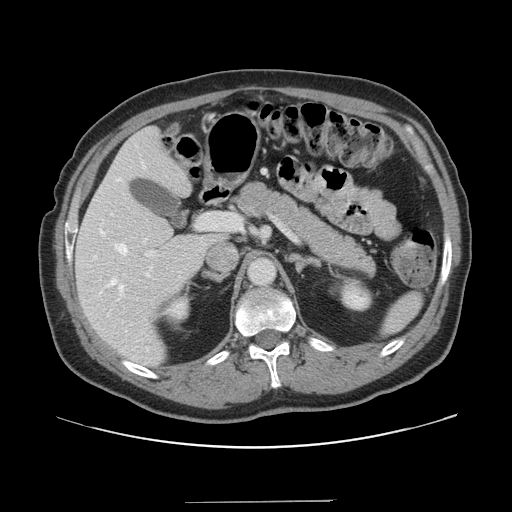
Contrast-enhanced abdominal CT, one axial slice; slice 87 of 151 in the series (ordered by position); 120 kVp; soft-tissue window (W 400 / L 40 HU); 2.5 mm slice thickness; 512 × 512 image matrix, field of view 399 × 399 mm. Male patient, age 63 years. From the clinical record (not read from this slice): diagnosis: colorectal cancer liver metastases, imaged before liver resection.
Annotated regions visible in this slice (manually delineated by an expert):
- hepatic veins: bounding box <100,162,149,333> (left, top, right, bottom; pixels)
- liver: <76,129,221,367>
- planned liver remnant (the part of the liver to remain after resection): <76,129,221,367>
- portal vein (with intrahepatic branches): <145,213,242,257>